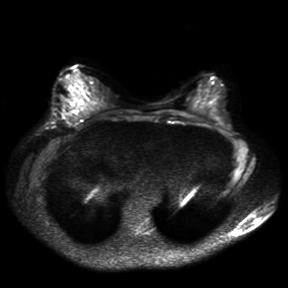
Breast MRI, one axial slice; slice 16 of 30 in the series (ordered by position); diffusion-weighted series; image 2 of 4 stored at this slice position (different b-values; order by instance number); 3 T; 4 mm slice thickness; 288 × 288 image matrix. Female patient.
Annotated regions visible in this slice (expert manual segmentation):
- tumour on diffusion-weighted imaging: box from (x=63, y=111) to (x=75, y=123) px